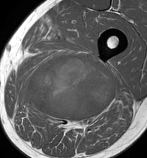
MRI of an extremity soft-tissue mass, one axial slice. Slice 64 of 86 in the series (ordered by position). MR volume resampled by the dataset authors to the PET/CT grid (not the native acquisition matrix). 3.27 mm slice thickness. 147 × 158 image matrix. Male patient. Case-level facts recorded for this patient, not image findings: histological type: undifferentiated pleomorphic liposarcoma; grade: high; site of the primary tumour: left thigh.
Annotated regions visible in this slice (expert contour drawn on MRI and transferred to this co-registered scan by the dataset authors):
- gross tumour volume including surrounding oedema: bounding box <16,54,115,130> (left, top, right, bottom; pixels)
- gross tumour volume (mass): <25,54,115,120>